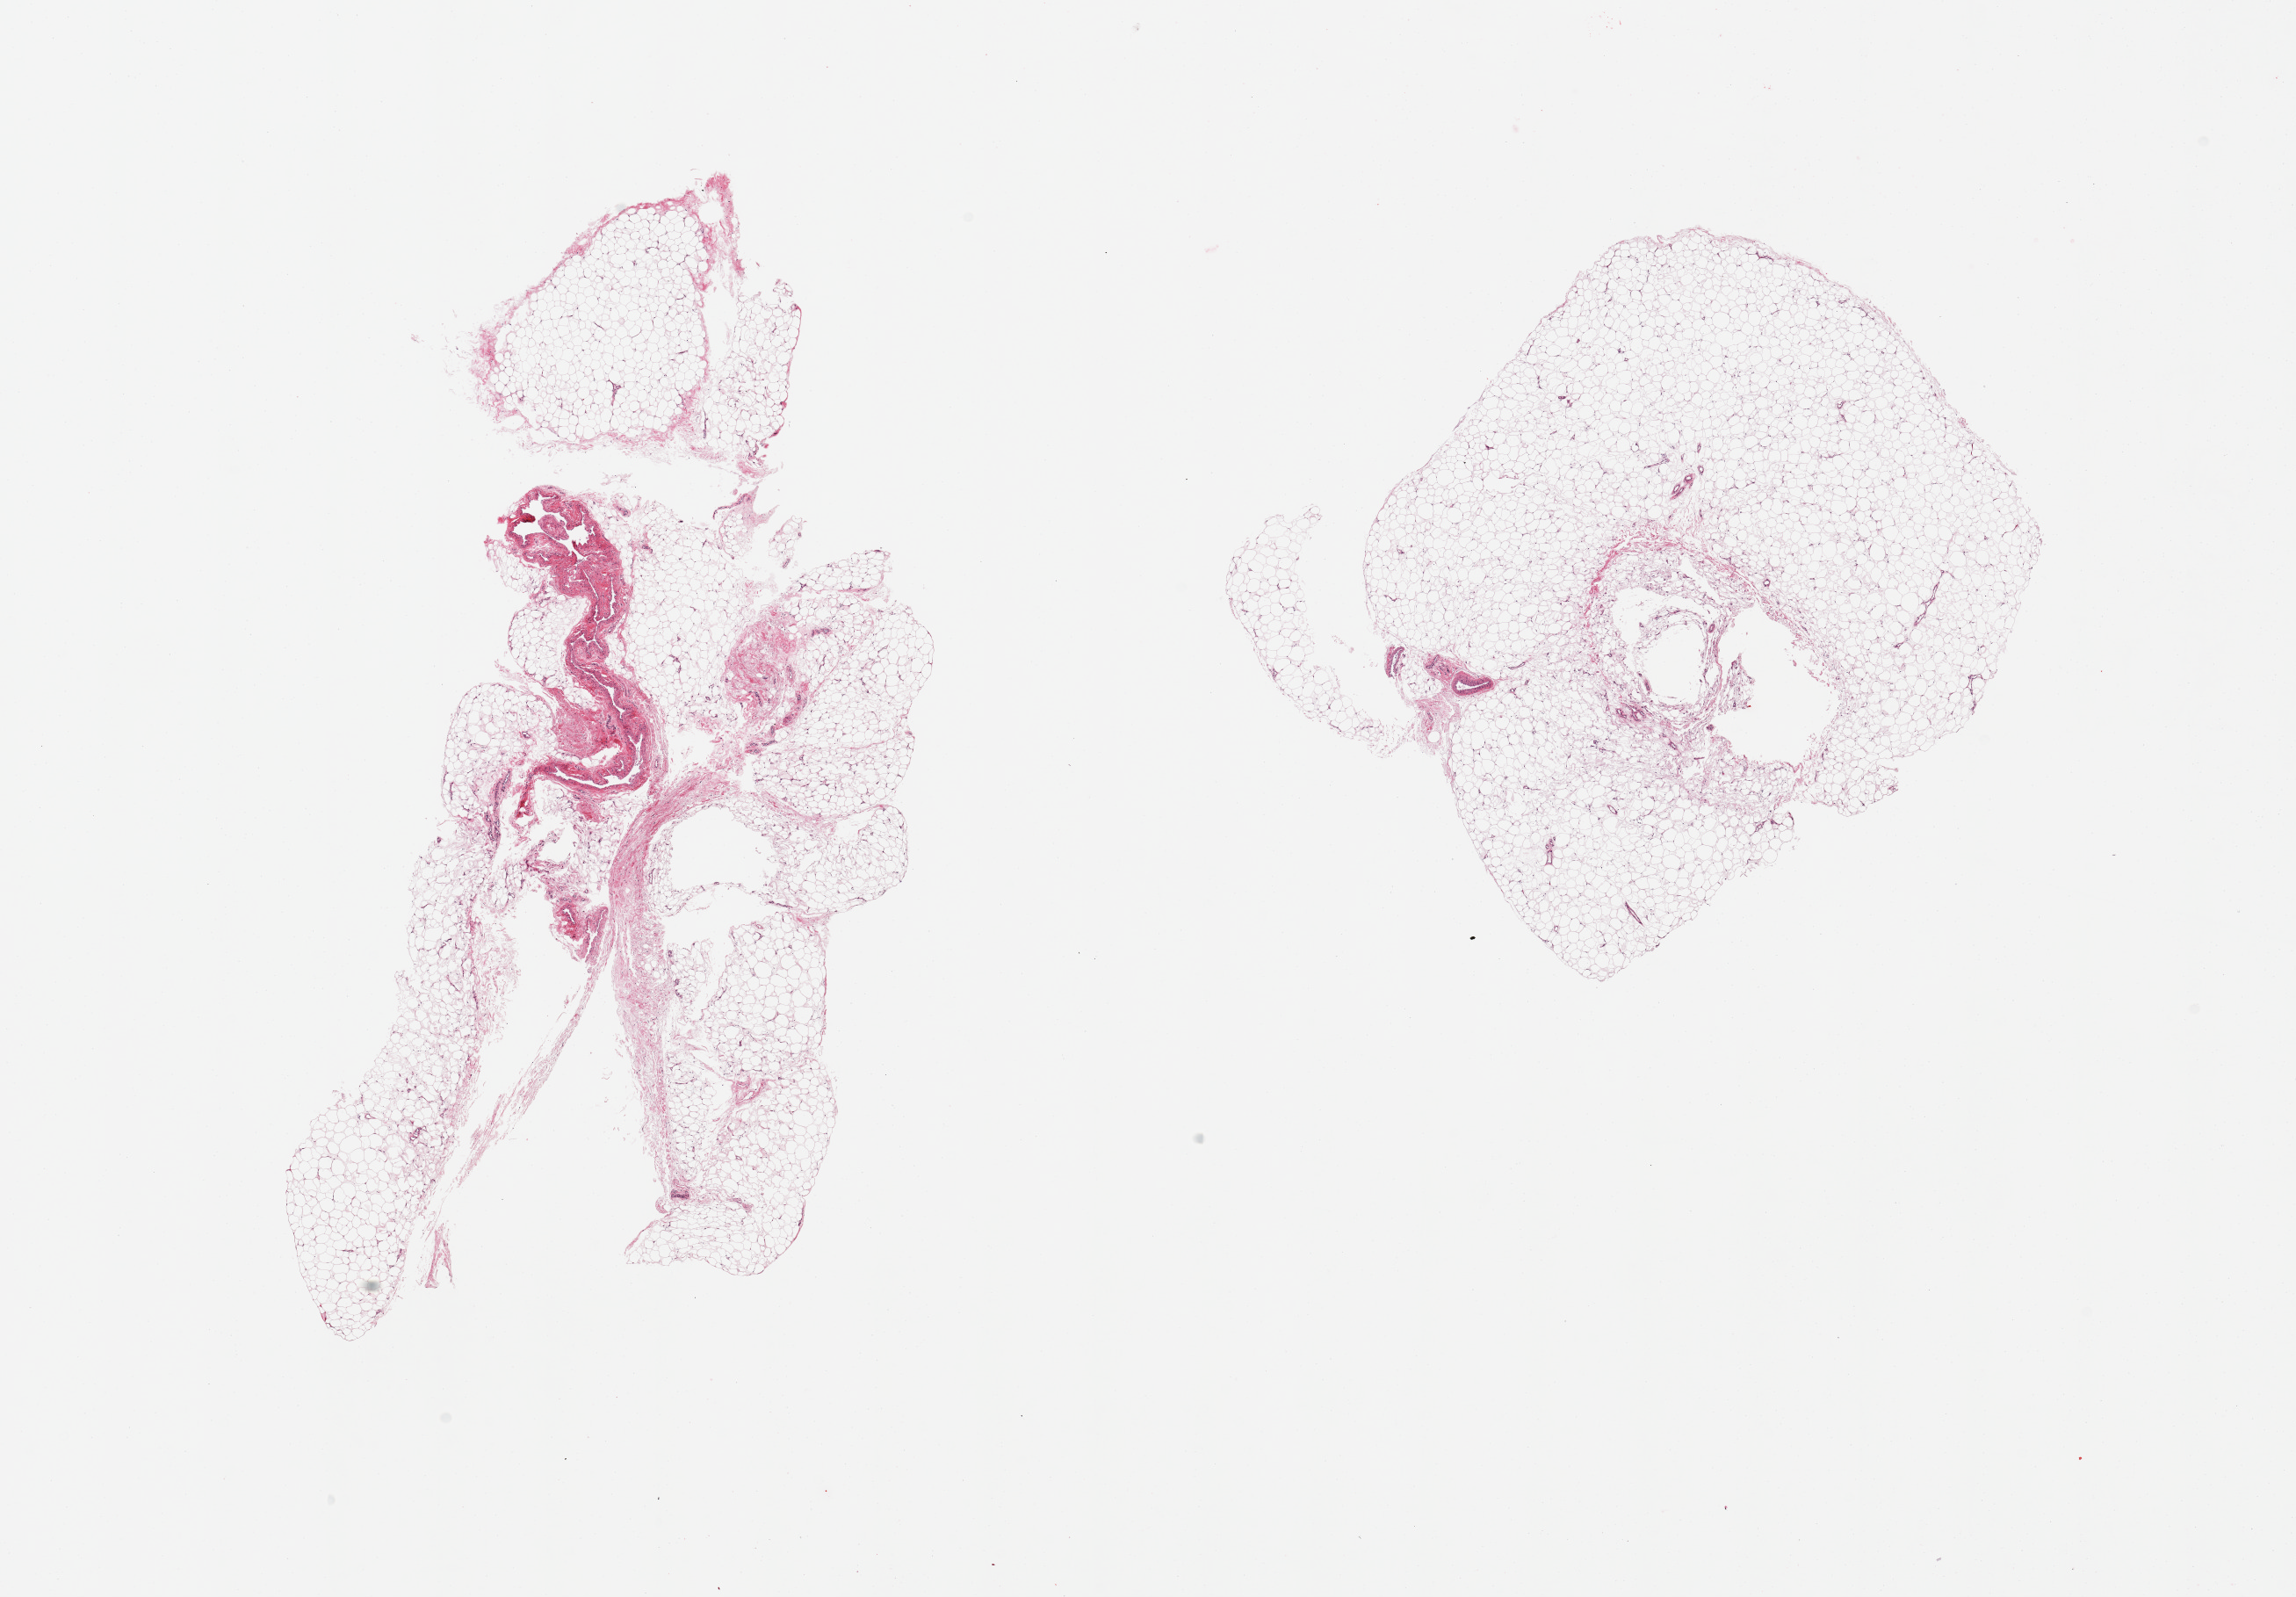
Hematoxylin and eosin (H&E) whole-slide image, brightfield — low-resolution overview of the scanned area, about 20.7 x 14.4 mm. PAXgene-fixed paraffin-embedded (PFPE) section. Section of adipose tissue (target tissue). Tissue donor sample. Donor sex: male.
Review note (as recorded): 2 pieces, ~10% fascia/vascular elements.